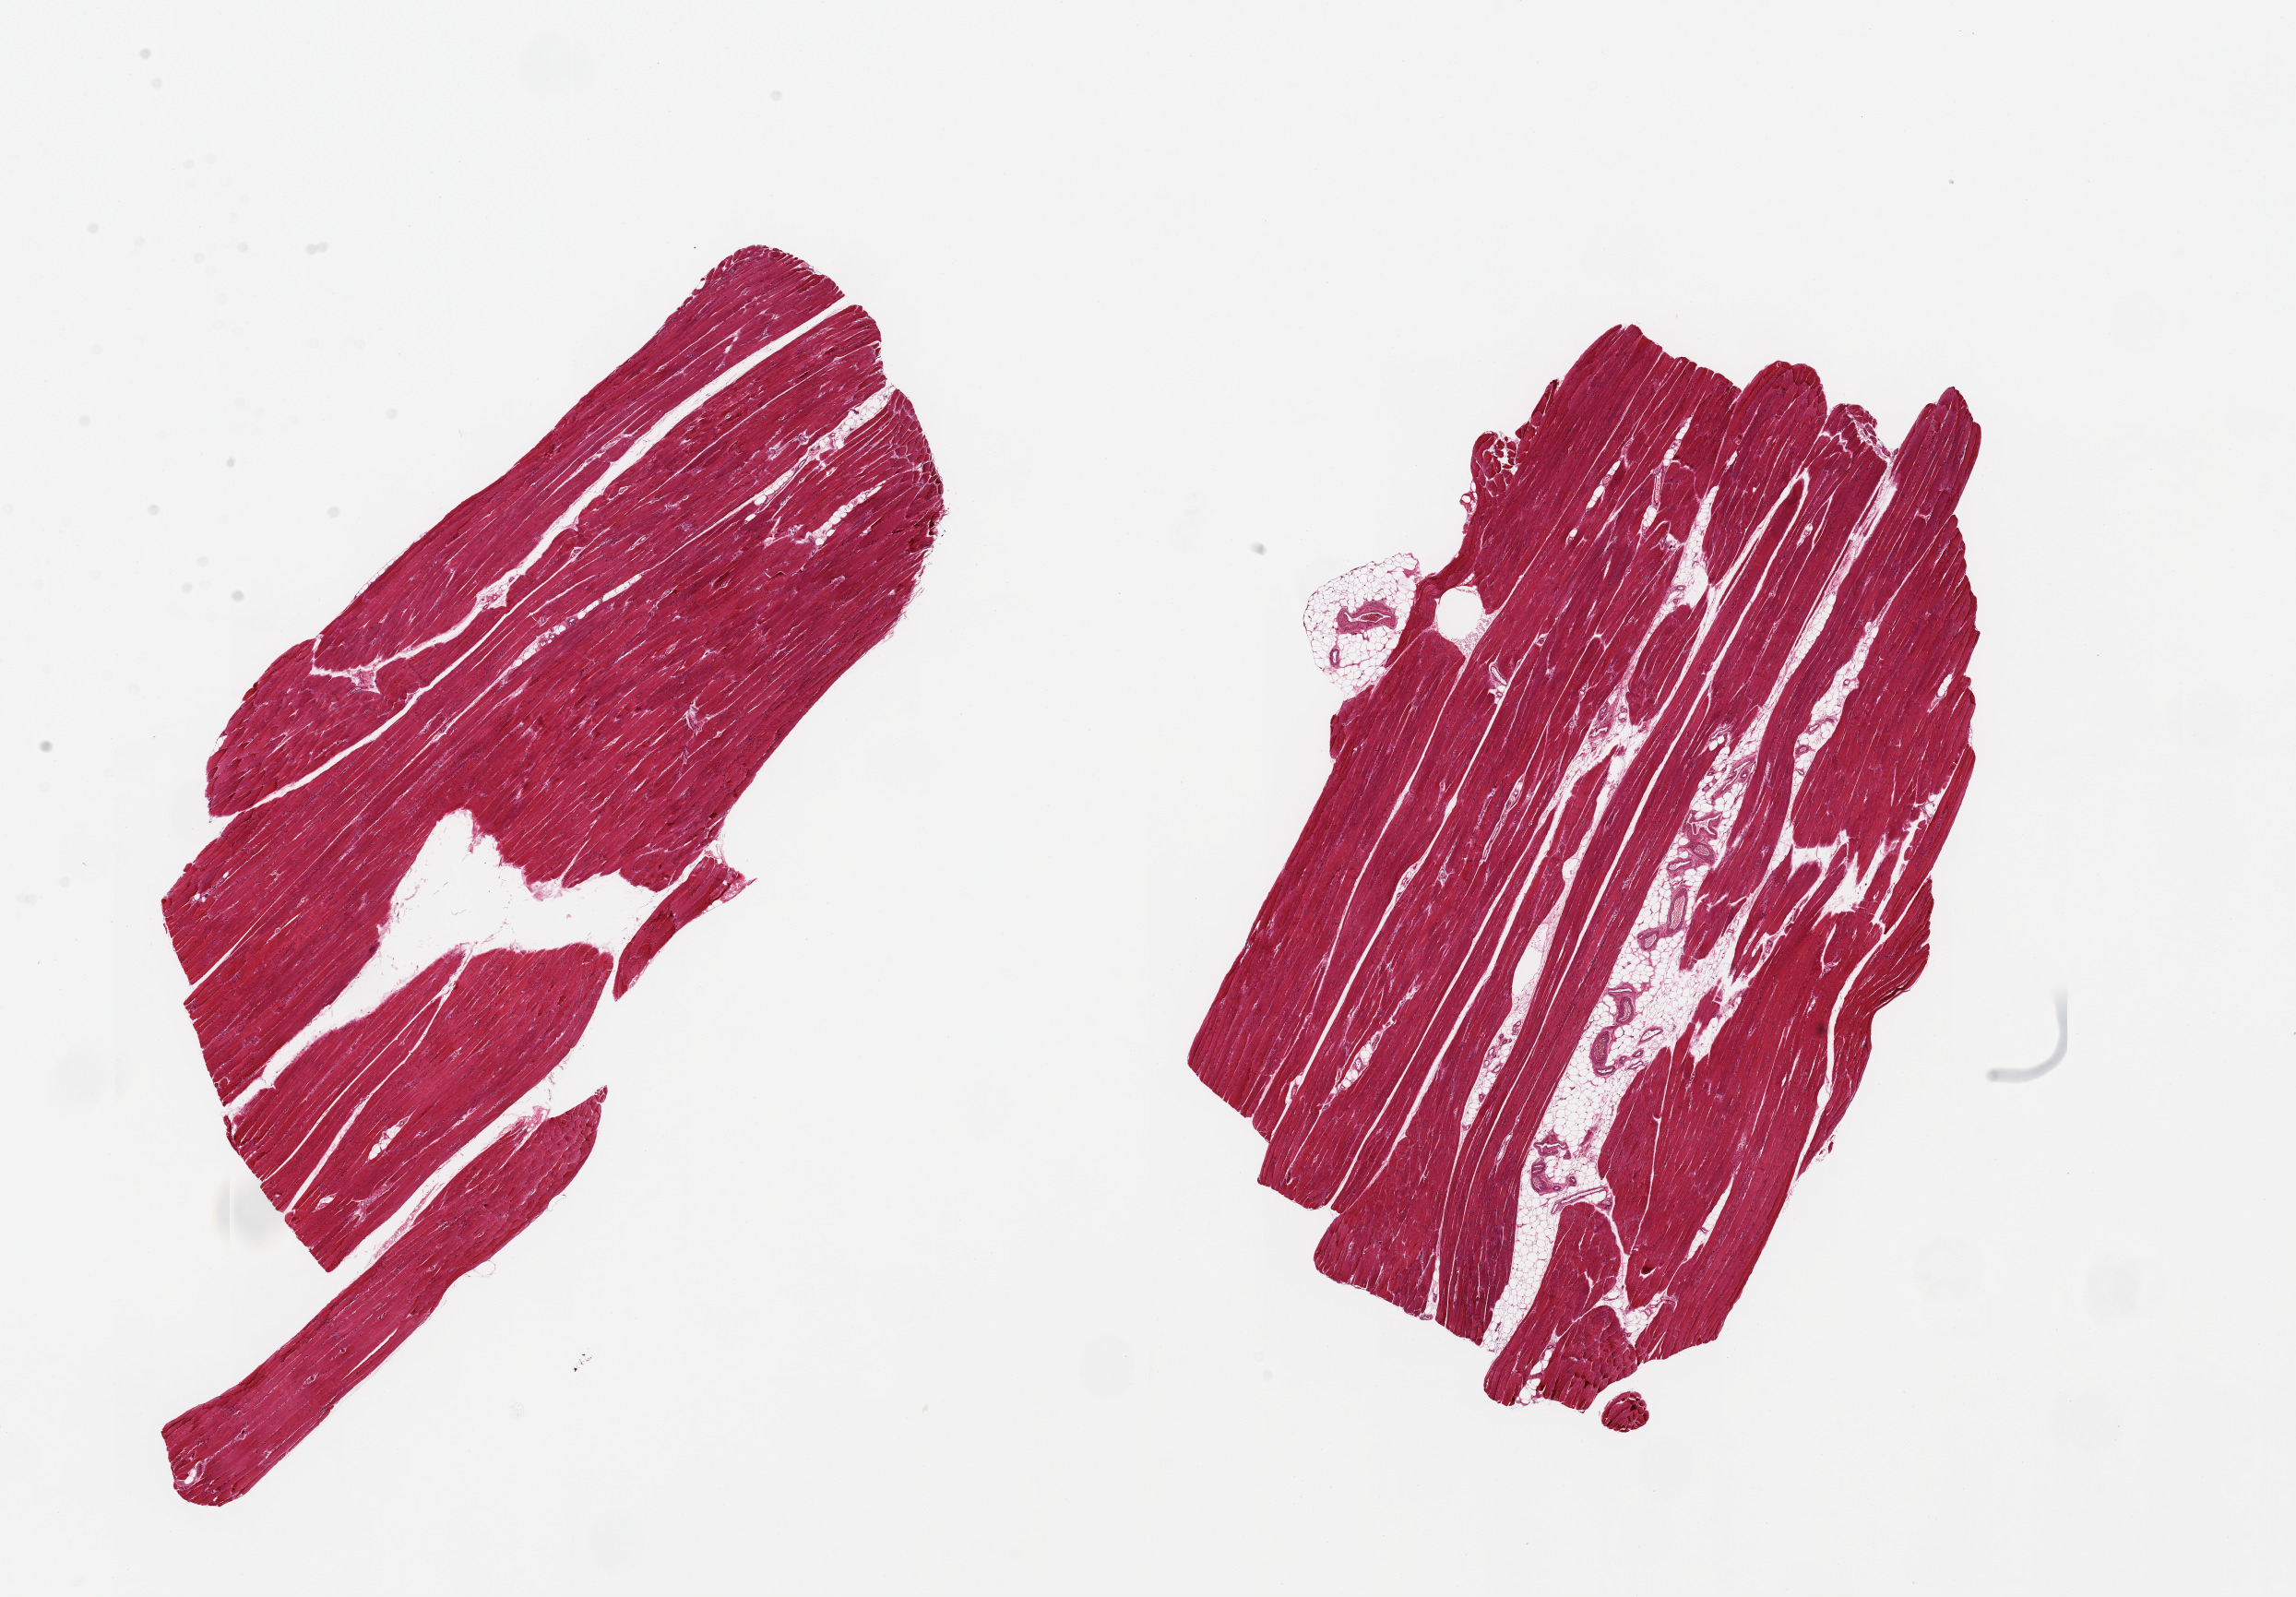
Digitized H&E-stained section — low-resolution overview of the scanned area, about 19.7 x 13.7 mm (from a 20x scan), PAXgene-fixed paraffin-embedded (PFPE) section, sampled site (target tissue): skeletal muscle, donor tissue sample. Male donor.
Pathologist's review note for this sample: 2 pieces; ~10% internal fat.